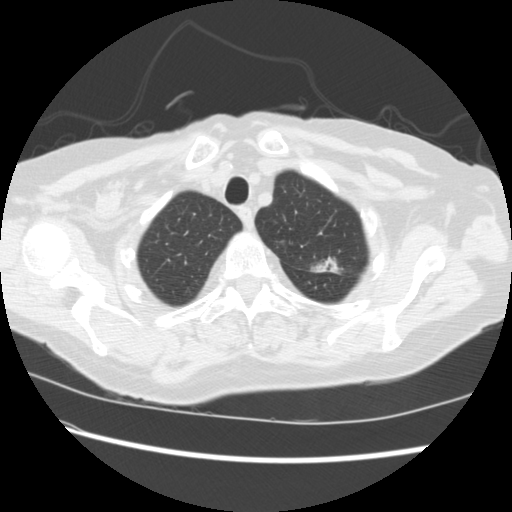
Low-dose screening chest CT, one axial slice. Position 189 of 224 along the scan axis. Reconstruction kernel STANDARD. 120 kVp. Lung window (W 1500 / L -600 HU). 2.5 mm slice thickness. 512 × 512 image matrix, field of view 340 × 340 mm.
Annotated regions visible in this slice (expert manual segmentation):
- lesion 1 (tumor, upper lobe of left lung): bounding box (x1, y1, x2, y2) in pixels: (313, 258, 339, 273)